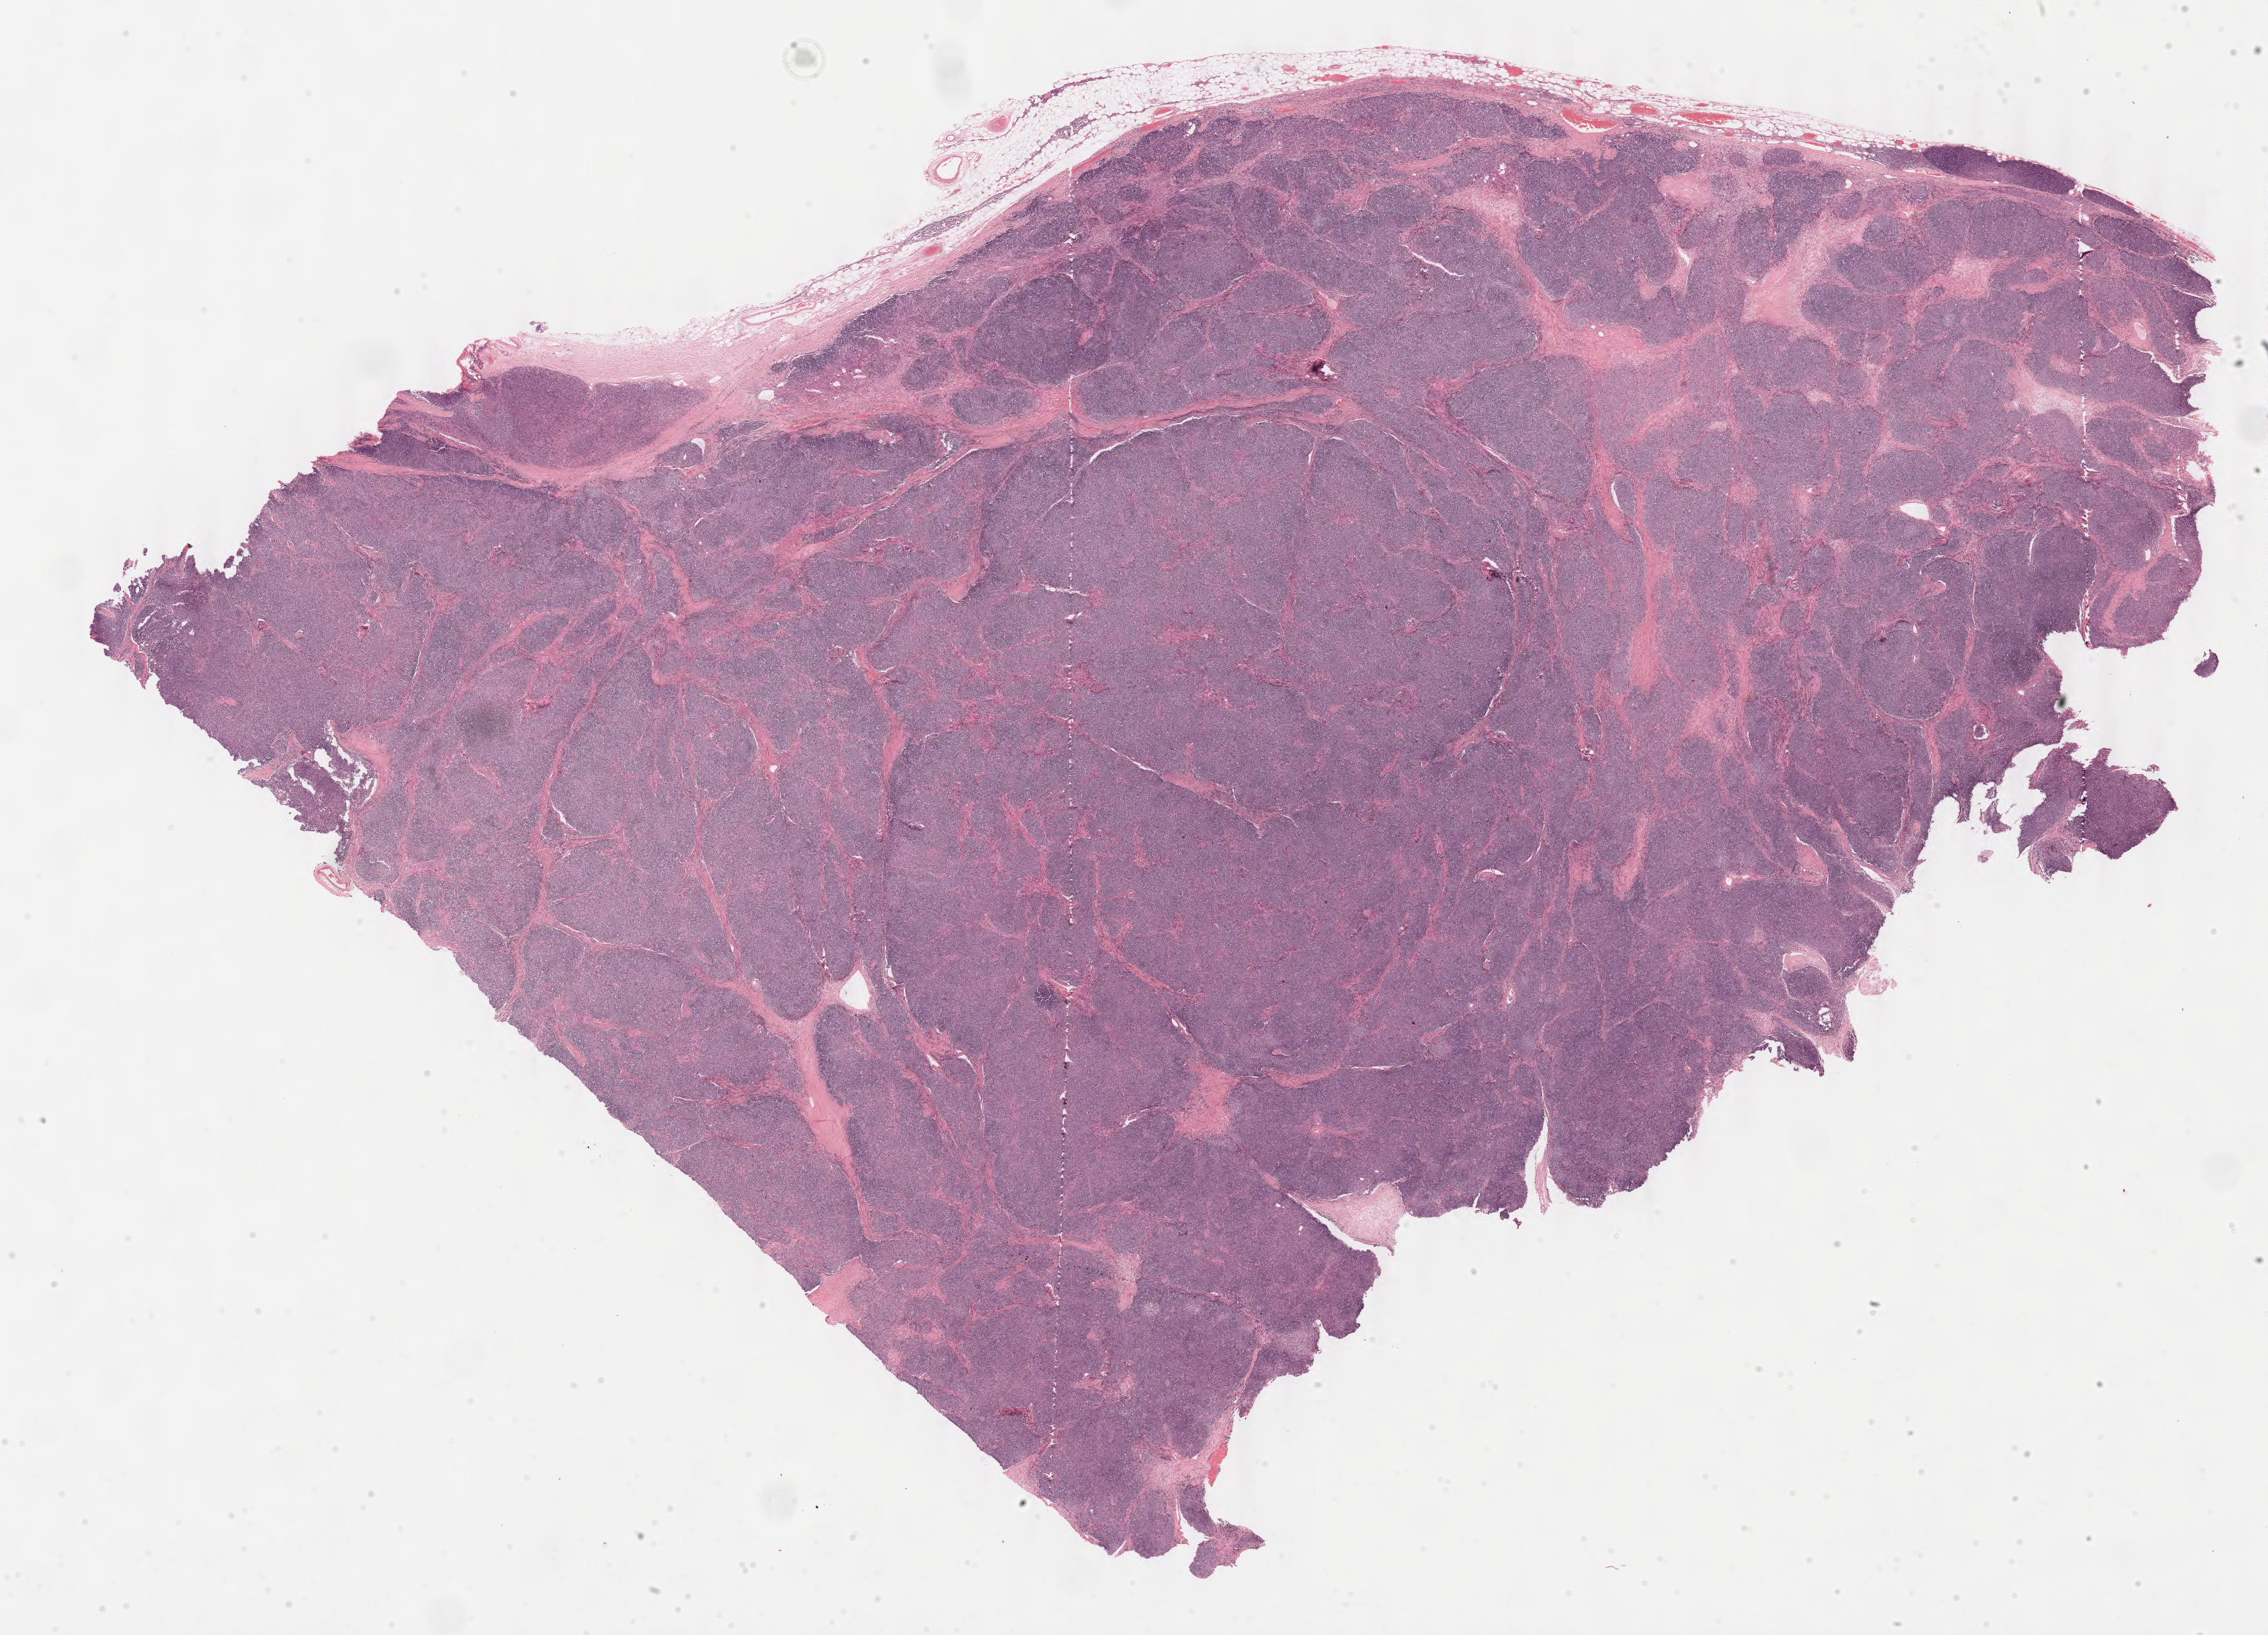
H&E whole-slide image — a low-resolution overview of the entire scanned area, about 24.6 x 17.7 mm; formalin-fixed paraffin-embedded (FFPE) diagnostic section; sample: primary tumour, thymus. Female, age 51 years at initial diagnosis.
Diagnosis: Thymoma, type AB, malignant.